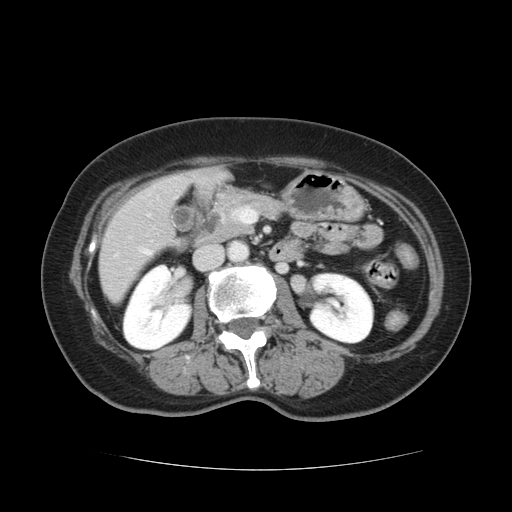
Contrast-enhanced abdominal CT, one axial slice. Intravenous contrast given. Soft-tissue window (W 400 / L 40 HU). 2.5 mm slice thickness. 512 × 512 image matrix. Female patient, age 67 years. Case-level facts recorded for this patient, not image findings: diagnosis: colorectal cancer liver metastases, imaged before liver resection; multiple liver metastases: yes; largest metastasis: 3 cm; chemotherapy before resection: no.
Structures marked on this image (expert manual segmentation):
- hepatic veins: bounding box [x1, y1, x2, y2] px = [145, 251, 148, 253]
- liver: [100, 169, 226, 302]
- planned liver remnant (the part of the liver to remain after resection): [100, 221, 172, 301]